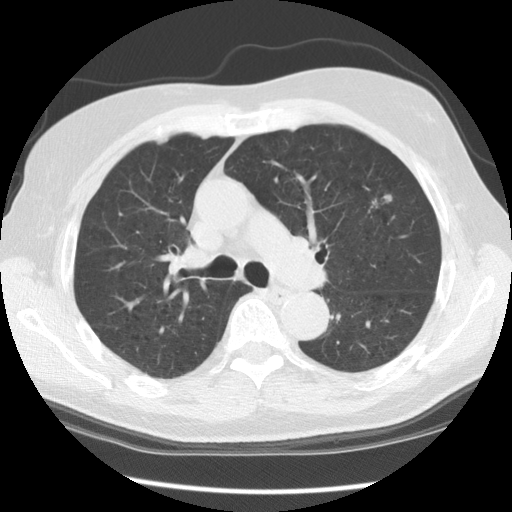
Low-dose screening chest CT, axial slice; second annual screen; lung window (W 1500 / L -600 HU); 140 kVp; slice 89 of 140 in the series; 512 × 512 image matrix, field of view 345 × 345 mm. Male, age 70 years at enrolment. Current smoker at enrolment.
Expert-annotated lung lesion, box from (x=343, y=182) to (x=404, y=237) px. The screening reader recorded 3 non-calcified nodules or masses ≥4 mm on this exam (right lower lobe, left upper lobe, left upper lobe); which of them this box marks is not recorded. Later outcome: lung cancer diagnosed 396 days after this screen (after the third annual screen) — adenocarcinoma, NOS, left upper lobe, moderately differentiated (G2), stage IIIA (AJCC 6th edition), 17 mm at pathology.